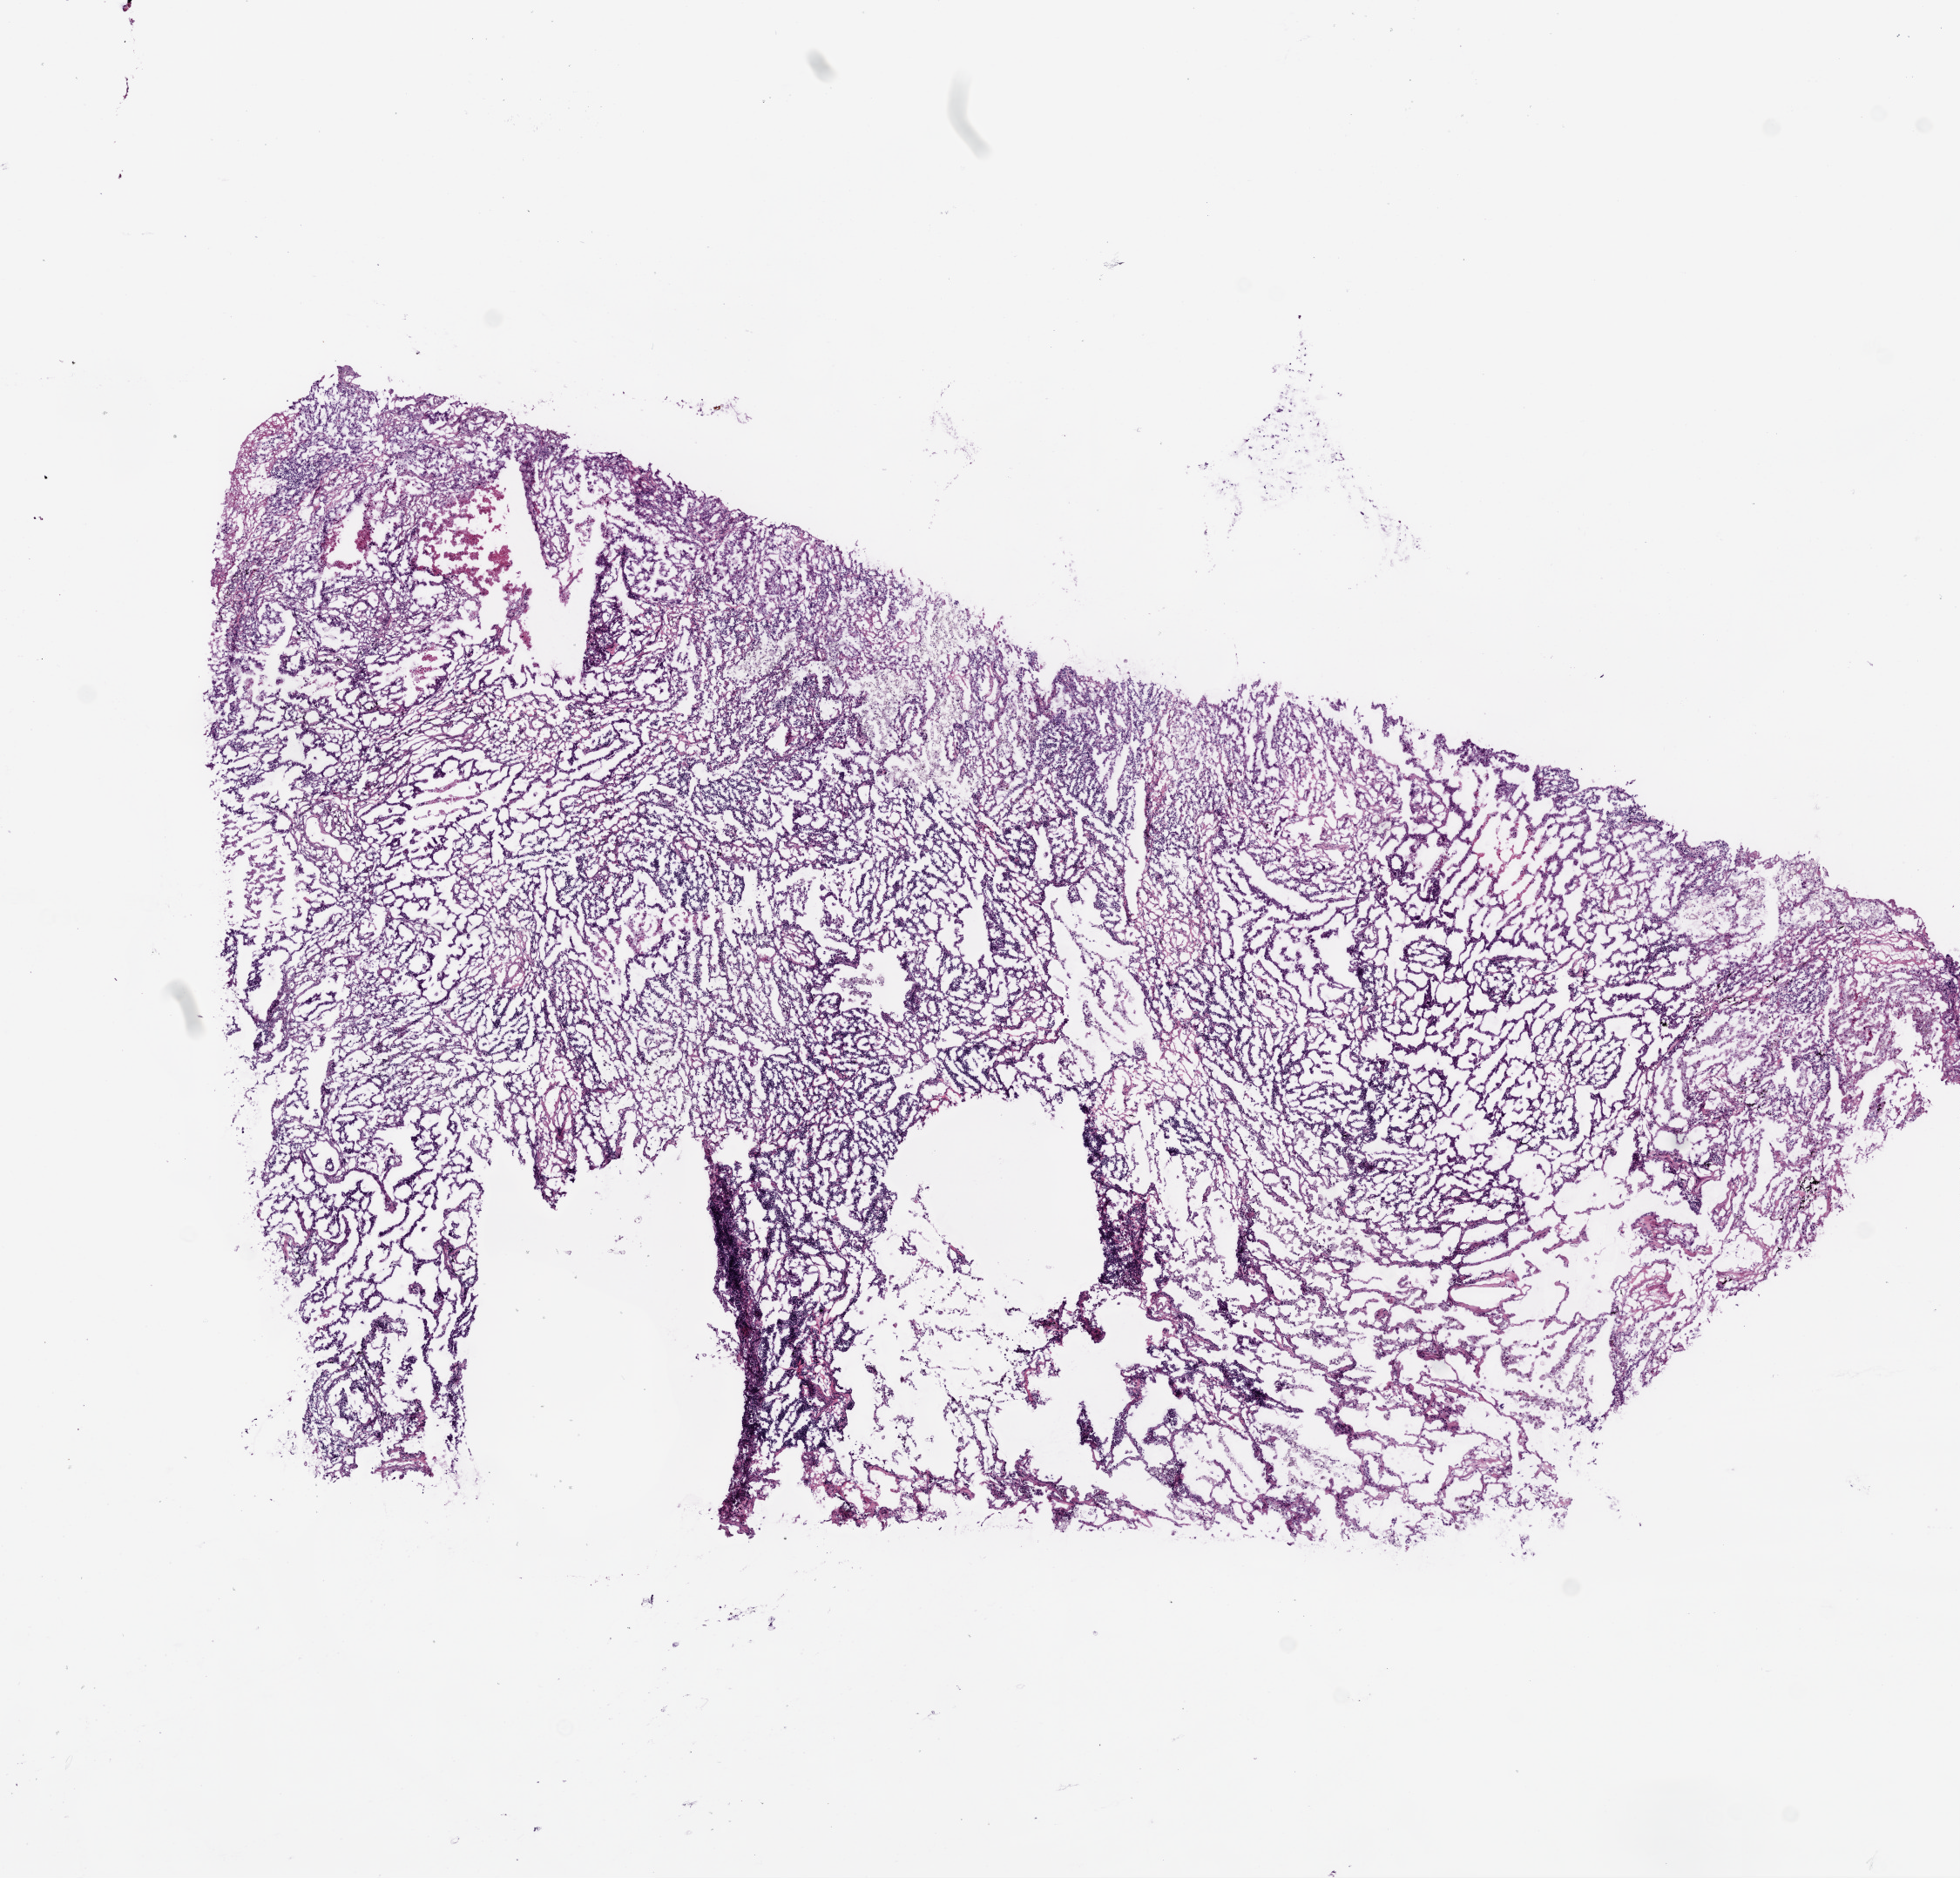
Whole-slide histology image, H&E — whole scanned area (about 9.0 x 8.6 mm, slide scanned at 20x) shown as a low-resolution overview, frozen section from the bottom of the tissue portion, sample: primary tumour, lung. Patient: female, age at initial diagnosis 72 years. Composition of this section per pathologist review: tumour cells 92%, tumour nuclei 65%, normal cells 0%, stromal cells 5%, necrosis 3%.
Histologic diagnosis: Adenocarcinoma, NOS (upper lobe, lung). TNM: T1 N0 M0. AJCC pathologic stage: IA.